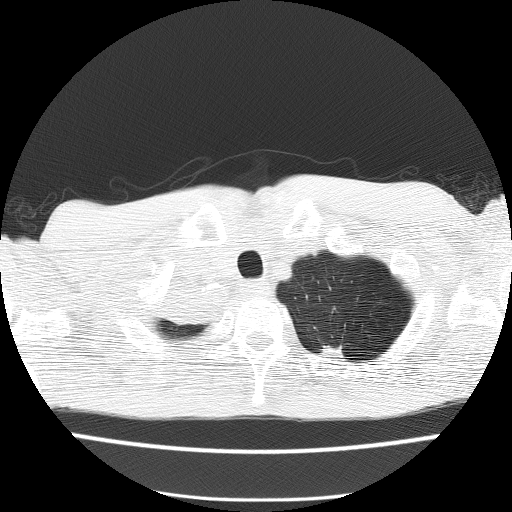
Low-dose screening chest CT, one axial slice. Position 133 of 150 along the scan axis. 120 kVp. Lung window (W 1500 / L -600 HU). 512 × 512 image matrix.
Outlined on this slice (manually delineated by an expert):
- lesion 1 (tumor, hilum of right lung): box from (x=166, y=287) to (x=213, y=323) px